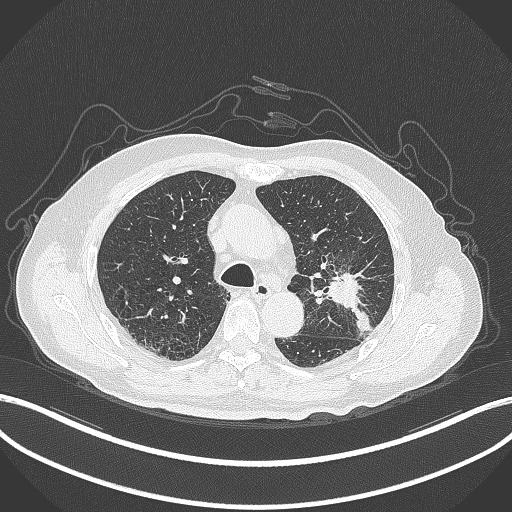
Chest CT, one axial slice; slice 196 of 331 in the series (ordered by position); reconstruction kernel B70f; 120 kVp; lung window (W 1500 / L -600 HU); 1 mm slice thickness; 512 × 512 image matrix, field of view 400 × 400 mm. Patient: male, 79 years. Case-level facts recorded for this patient, not image findings: clinical TNM (as recorded): T2a N1 M1.
Structures marked on this image (bounding box drawn by a radiologist):
- lung tumour (recorded histology: adenocarcinoma): box from (x=329, y=273) to (x=376, y=340) px